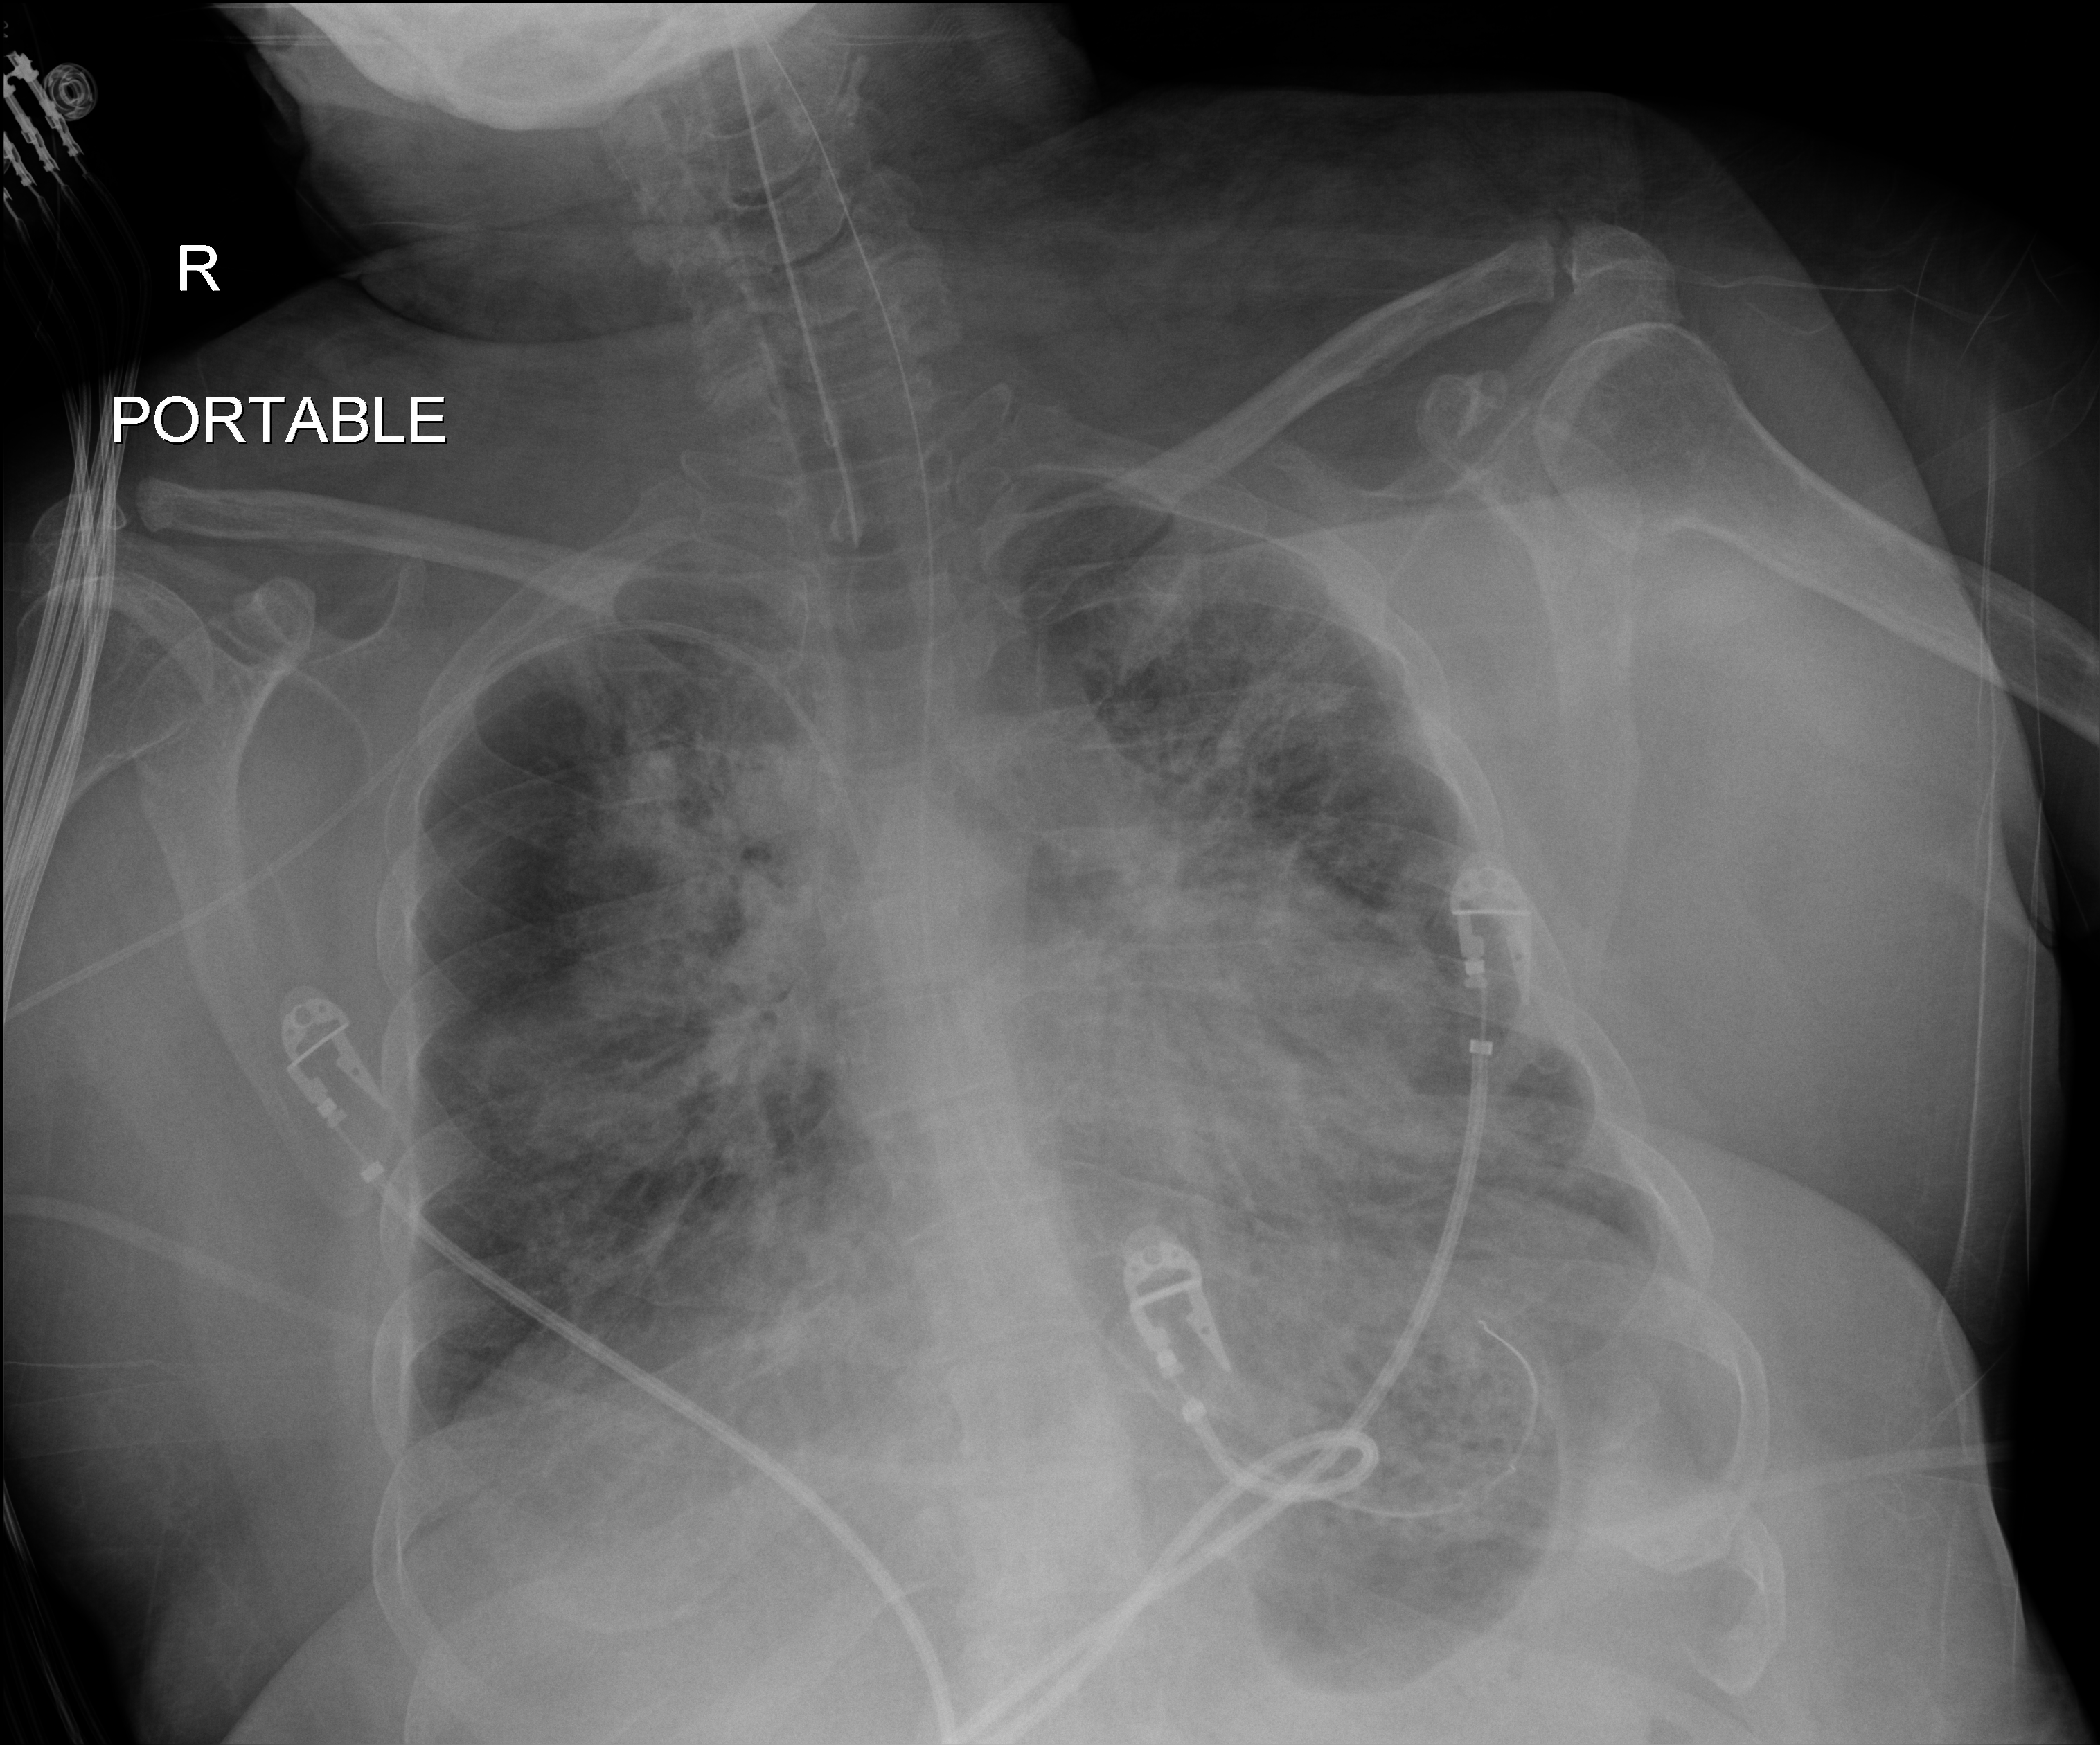
Chest radiograph; anteroposterior (AP) projection. Patient hospitalised with COVID-19, aged 18–59 years.
Admission-level facts for this patient (not findings on this image; timing relative to this image not recorded):
- mechanically ventilated during this hospital stay: yes
- length of hospital stay: 15 days
- admitted to intensive care during this hospital stay: yes